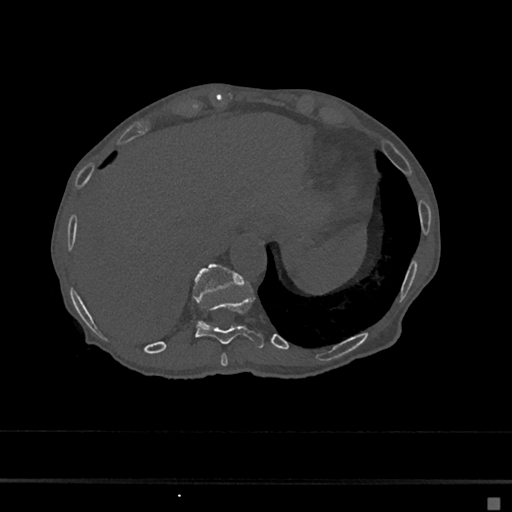
CT including the spine, one axial slice. Position 215 of 797 along the scan axis. Reconstruction kernel Br40s/3. 120 kVp. Bone window (W 1800 / L 400 HU). 0.5 mm slice thickness. 512 × 512 image matrix, field of view 360 × 360 mm. Patient: female, 68 years. From the clinical record (not read from this slice): primary cancer: renal.
Annotated regions visible in this slice (semi-automatically segmented with operator editing):
- T10 vertebra: box from (x=195, y=295) to (x=264, y=348) px
- T11 vertebra: (x=193, y=263)–(x=245, y=326)
- T9 vertebra: (x=220, y=353)–(x=228, y=367)